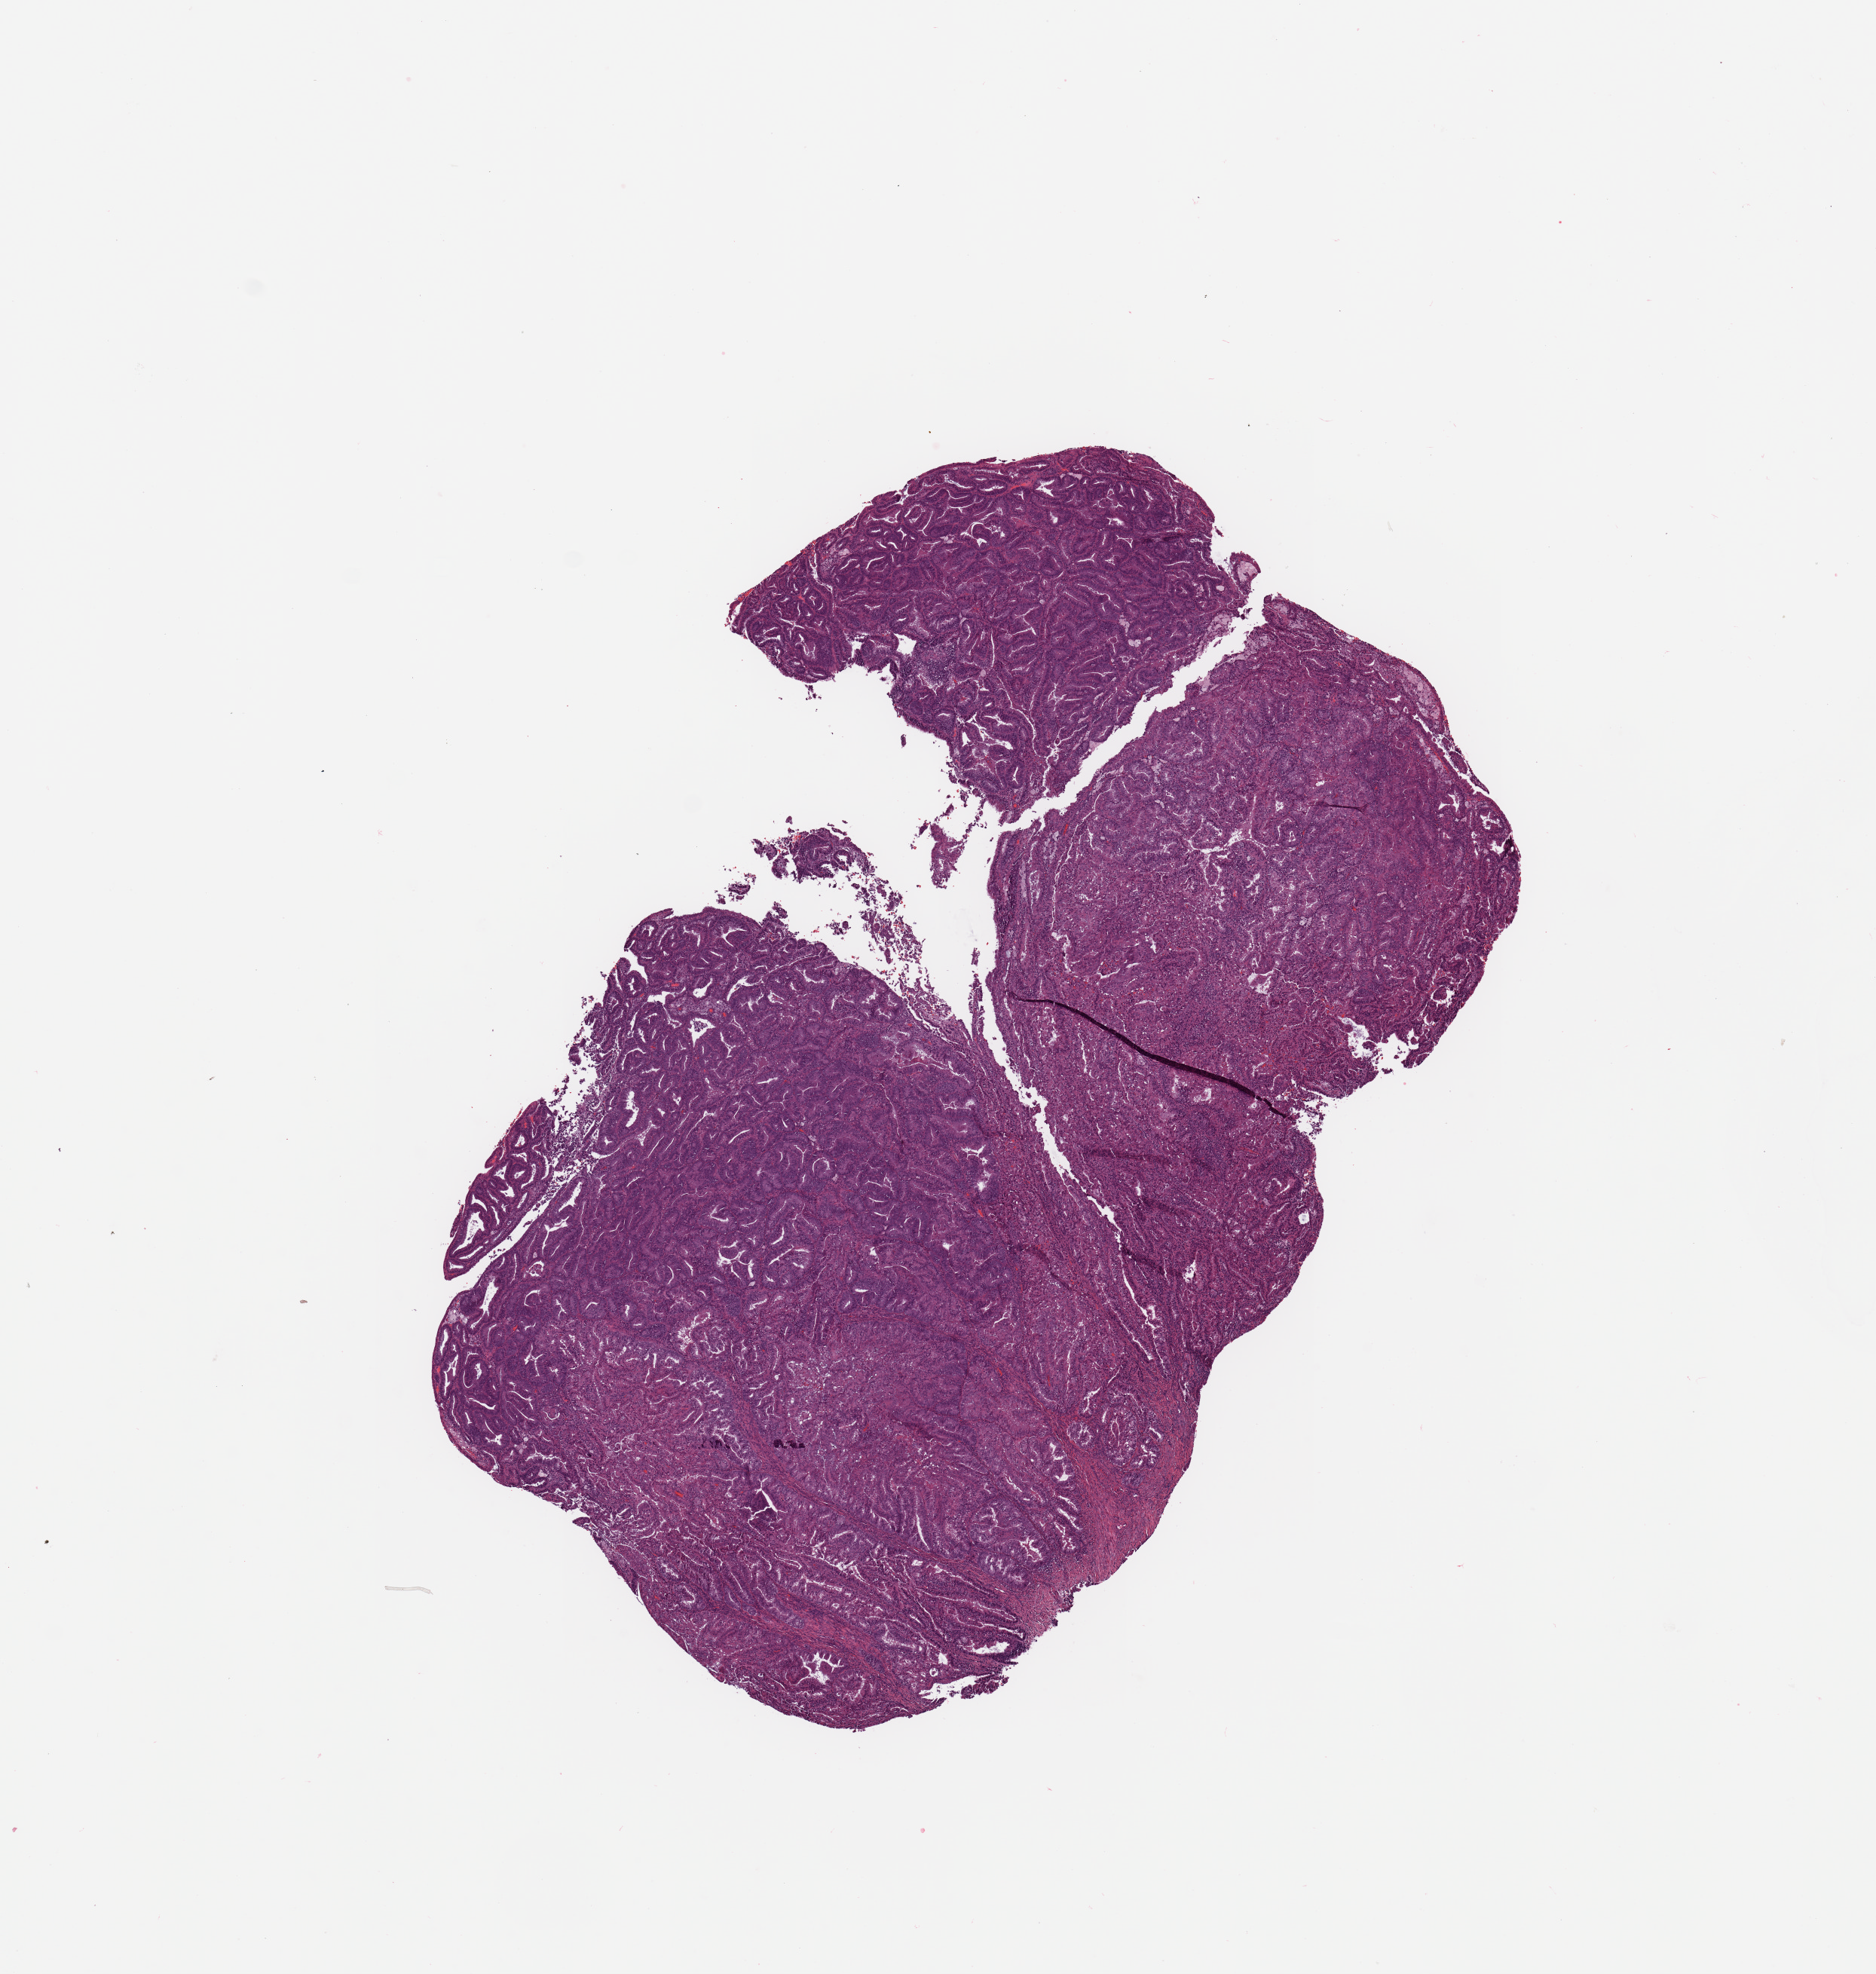
H&E-stained whole-slide image, whole scanned area (about 9.8 x 10.4 mm, acquisition: 20x scan) shown as a low-resolution overview, tumour tissue sample, sampled site: uterus. Female, 55 y/o. Histologic grade: G1 (well differentiated). Slide review estimates, as recorded: tumour nuclei 85%, necrosis 0%.
- histologic diagnosis: Endometrioid adenocarcinoma, NOS
- AJCC pathologic stage: I